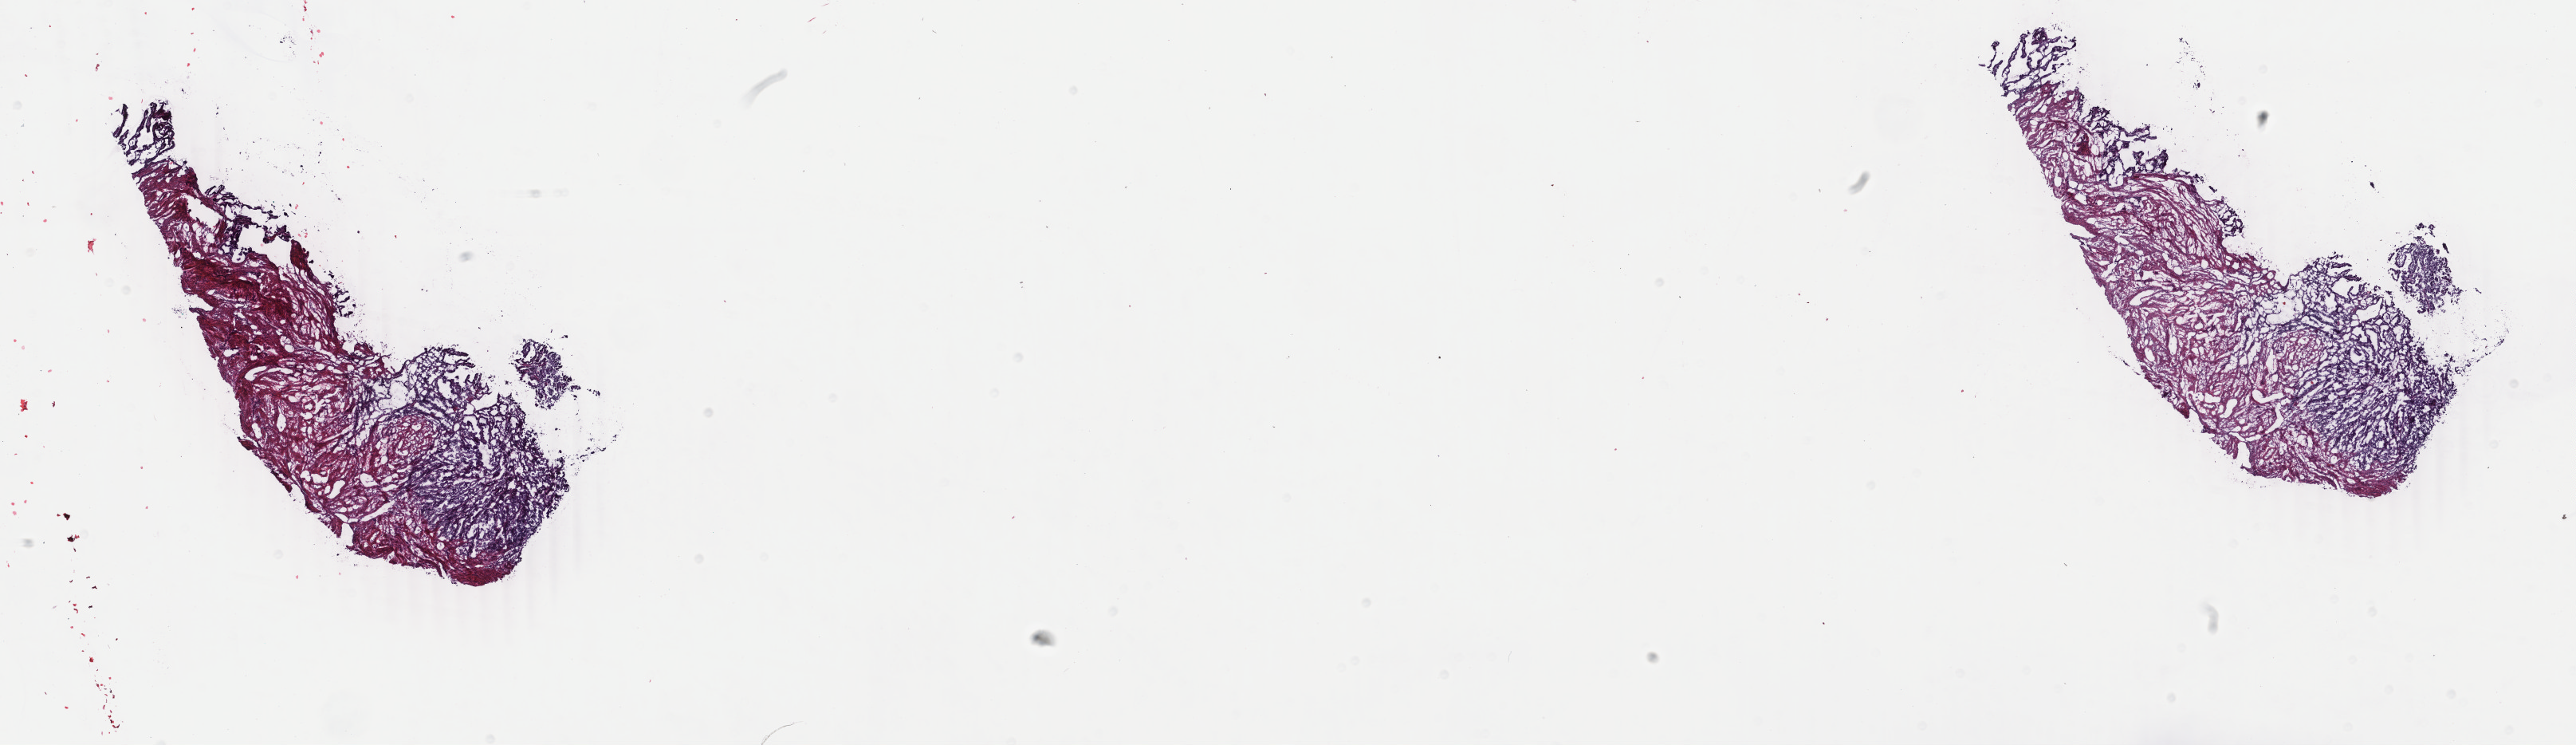
H&E-stained whole-slide image, low-resolution overview of the scanned area, about 25.7 x 7.4 mm; frozen section from the bottom of the tissue portion; sample: primary tumour, uterus. Female patient; age at initial diagnosis 33 years. Histologic grade: G3 (poorly differentiated). Composition of this section per pathologist review: tumour cells 40%, tumour nuclei 30%, normal cells 60%, stromal cells 0%, necrosis 0%. Infiltration values recorded for this section: lymphocyte infiltration 0%, monocyte infiltration 0%, neutrophil infiltration 0%.
* pathologic diagnosis: Endometrioid adenocarcinoma, NOS (endometrium)
* FIGO stage: IIIC2